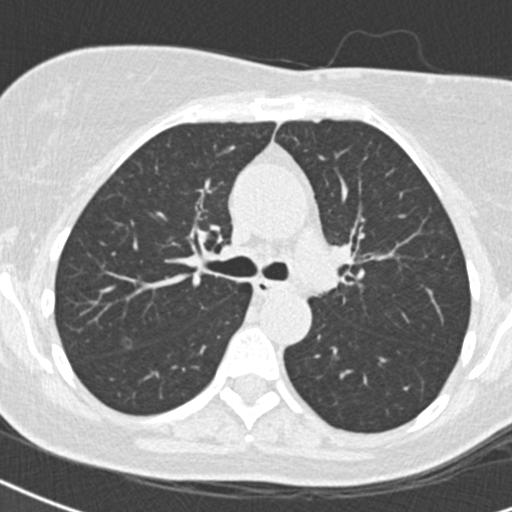
Low-dose screening chest CT, axial slice; baseline screening round; lung window (W 1500 / L -600 HU); standard (soft-tissue) reconstruction kernel (B30f). Female participant, aged 57 years at enrolment.
- Expert-annotated lung lesion, bounding box [x1, y1, x2, y2] px = [111, 331, 138, 356].
- Screening reader's record for this exam (one nodule recorded; not confirmed to be the boxed lesion): non-calcified nodule or mass ≥4 mm, left upper lobe, 10 × 9 mm, spiculated (stellate) margins, soft tissue attenuation.
- Note: the box lies in the patient's right hemithorax on this image, whereas the reader's record names the left lung; they may be different findings.
- Official screen result: positive, change unspecified: nodule(s) >= 4 mm or enlarging nodule(s), mass(es), or other non-specific abnormalities suspicious for lung cancer.
- Later outcome: lung cancer diagnosed 153 days after this screen — non-small cell carcinoma, right upper lobe, stage IA (AJCC 6th edition), 13 mm at pathology.